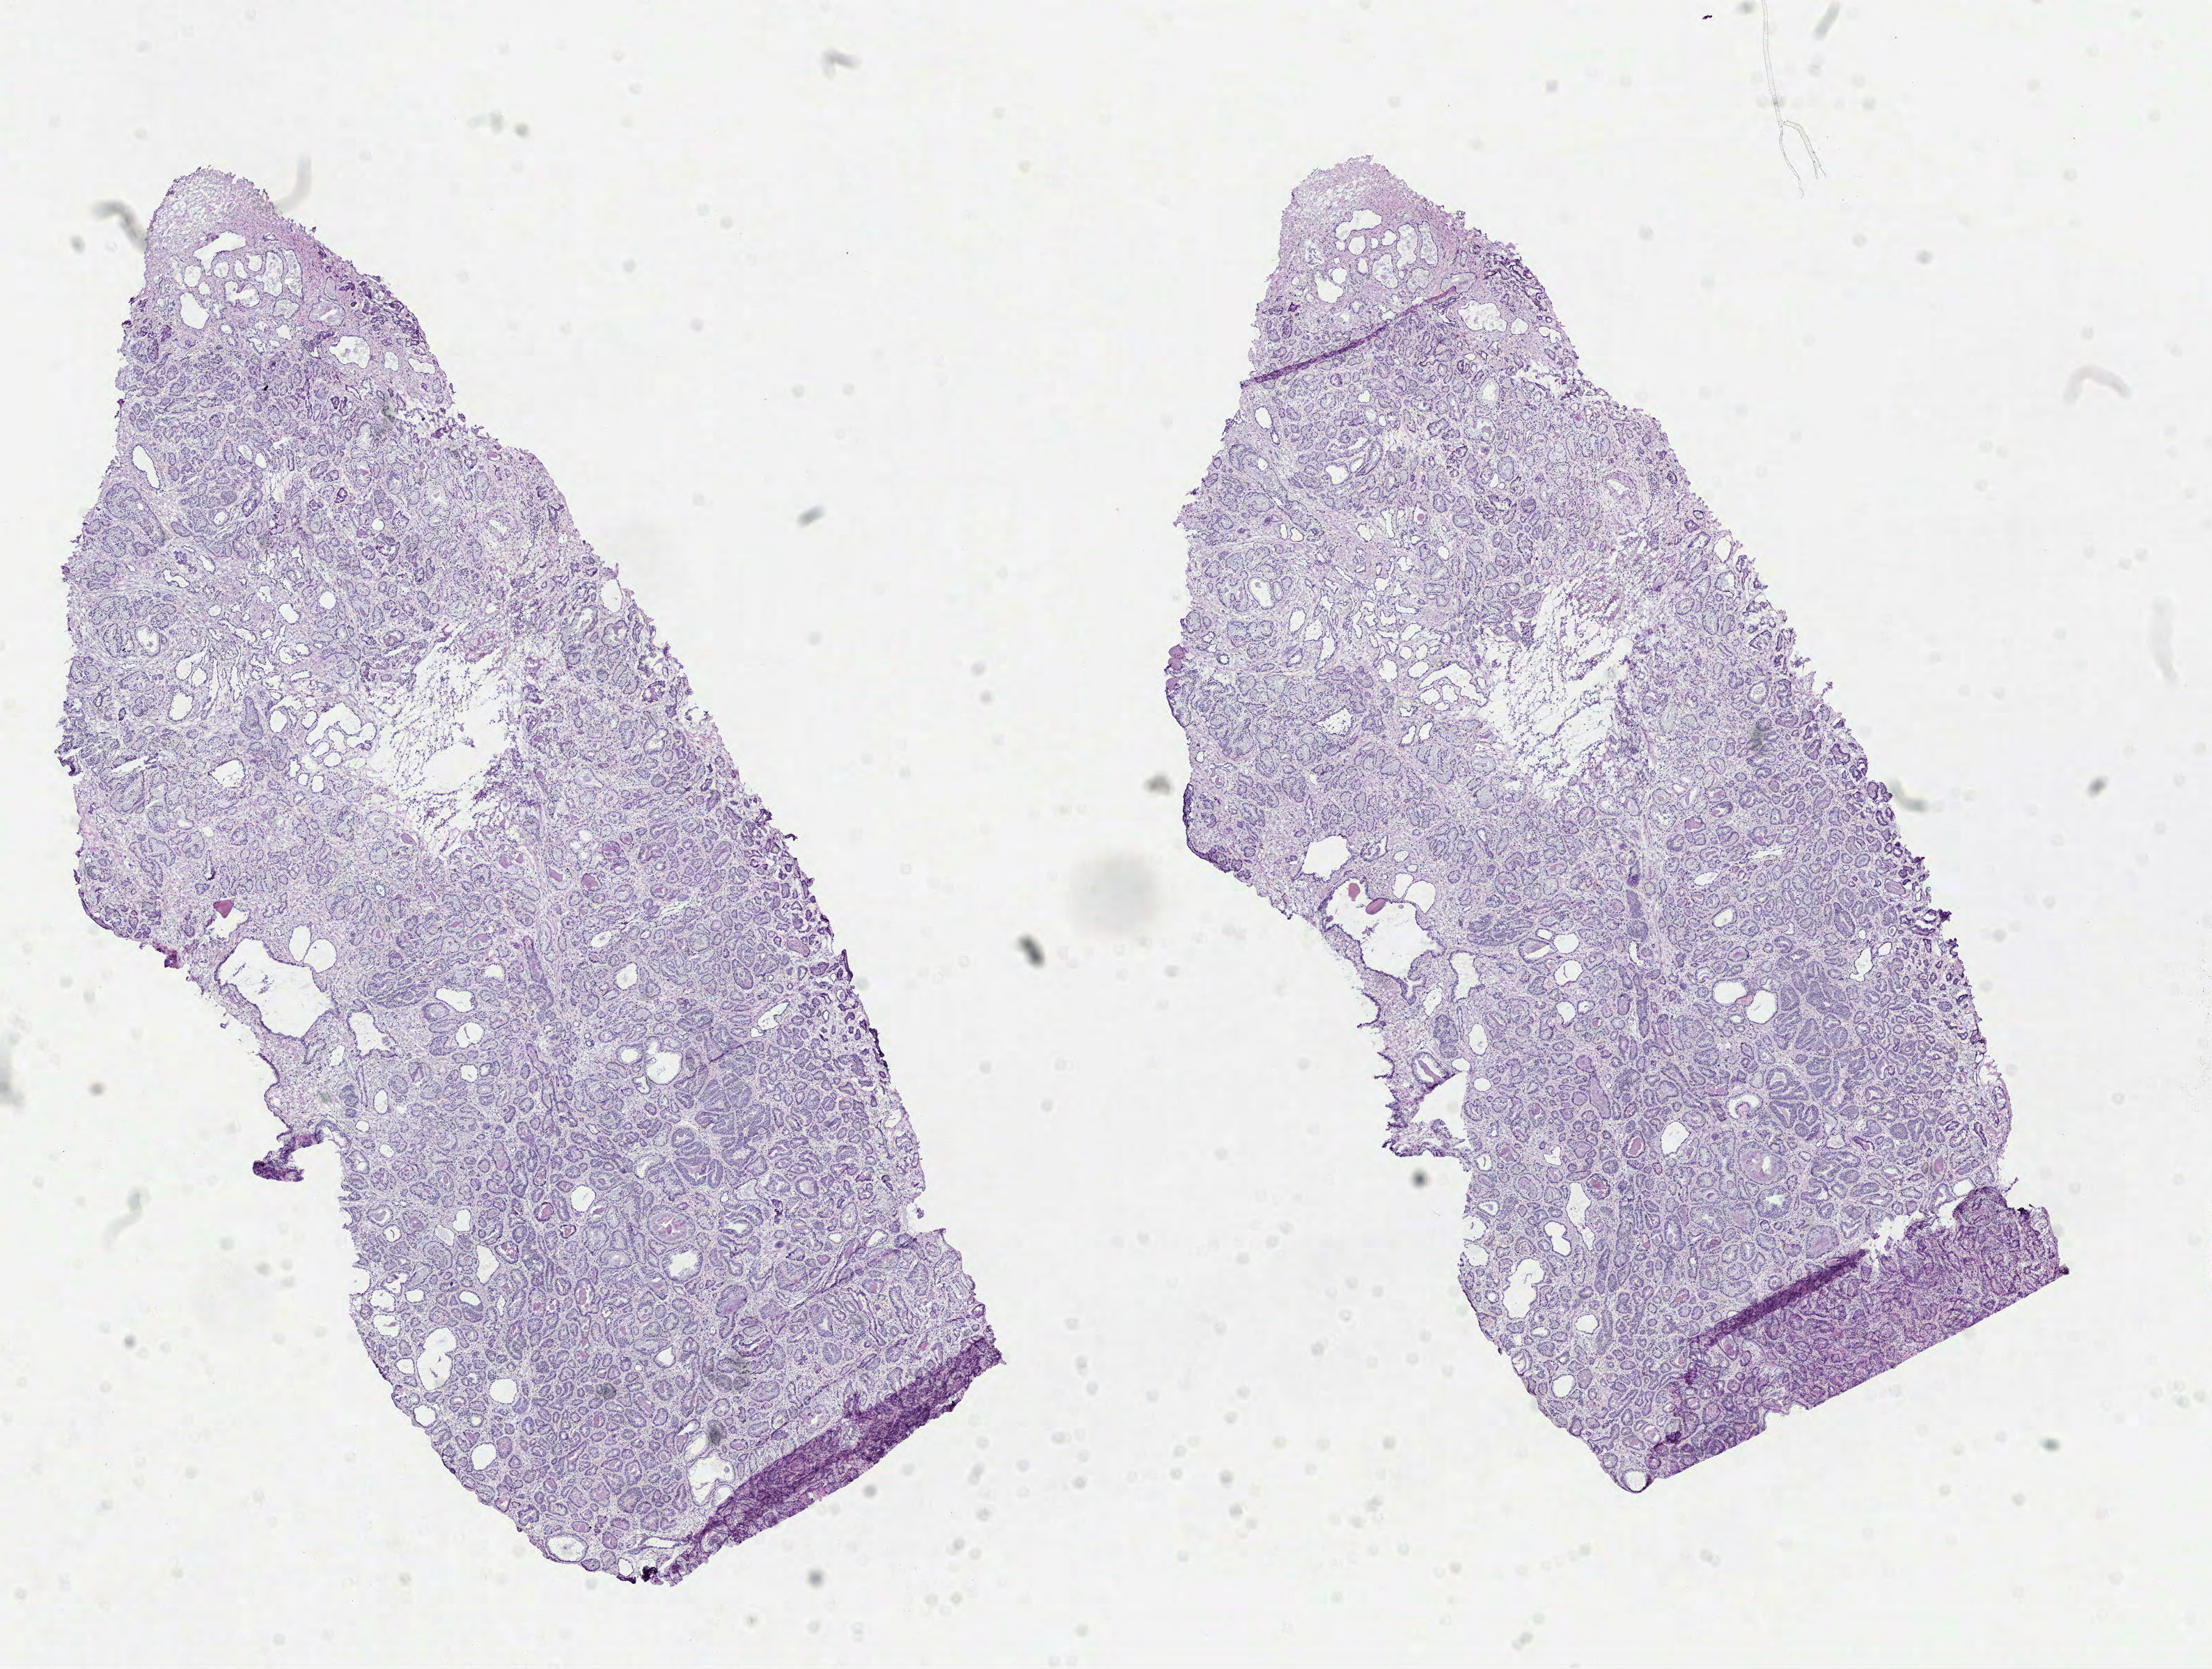
H&E-stained whole-slide image, shown as a low-resolution overview of the whole scanned area (about 12.8 x 9.7 mm). Formalin-fixed paraffin-embedded (FFPE) diagnostic section. Prostate, primary tumour sample. Male patient; age at initial diagnosis 66 years. Gleason score: 7 (4+3).
Diagnosis: Acinar cell carcinoma (prostate gland). Lymph nodes positive (case pathology): 0 of 19 examined.